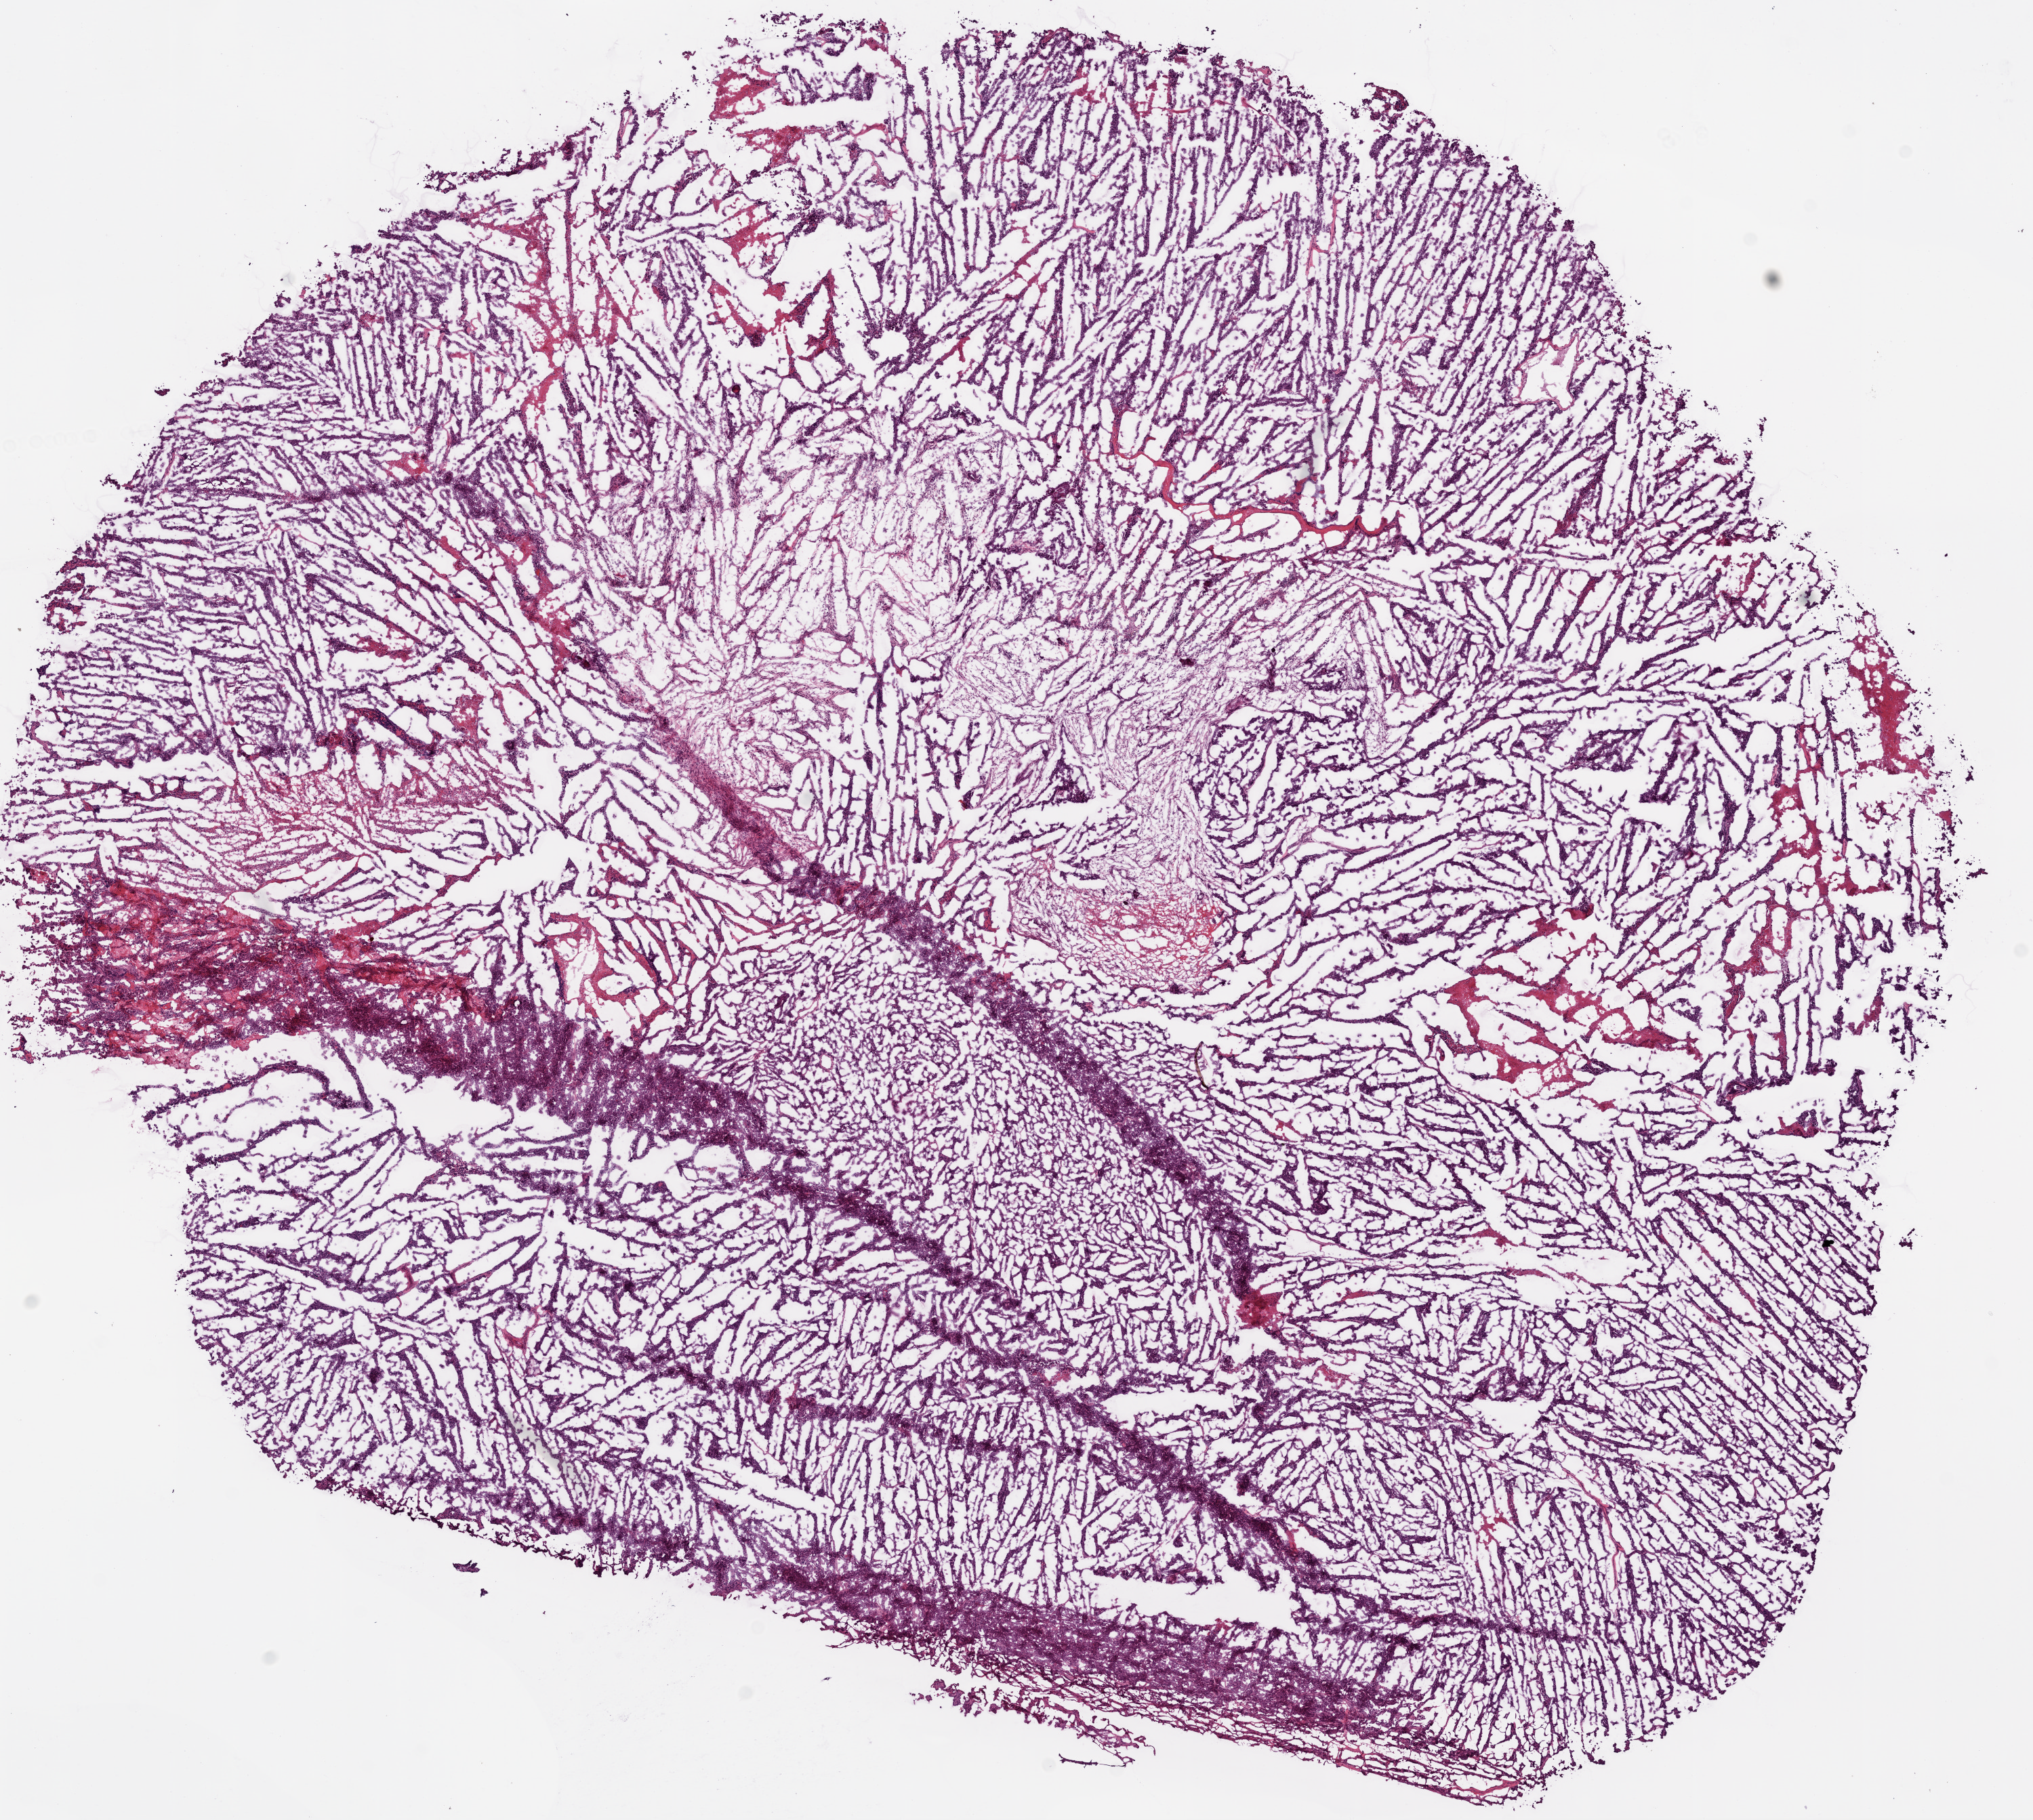
H&E-stained whole-slide image, shown as a low-resolution overview of the whole scanned area (about 12.0 x 10.8 mm, from a 20x scan). Frozen section. Sample: primary tumour, ovary. Female patient; age at initial diagnosis 47 years. Histologic grade: G3 (poorly differentiated). Slide review estimates, as recorded: tumour cells 85%, tumour nuclei 95%, normal cells 0%, stromal cells 5%, necrosis 10%.
• FIGO stage: IIIC
• histologic diagnosis: Serous cystadenocarcinoma, NOS